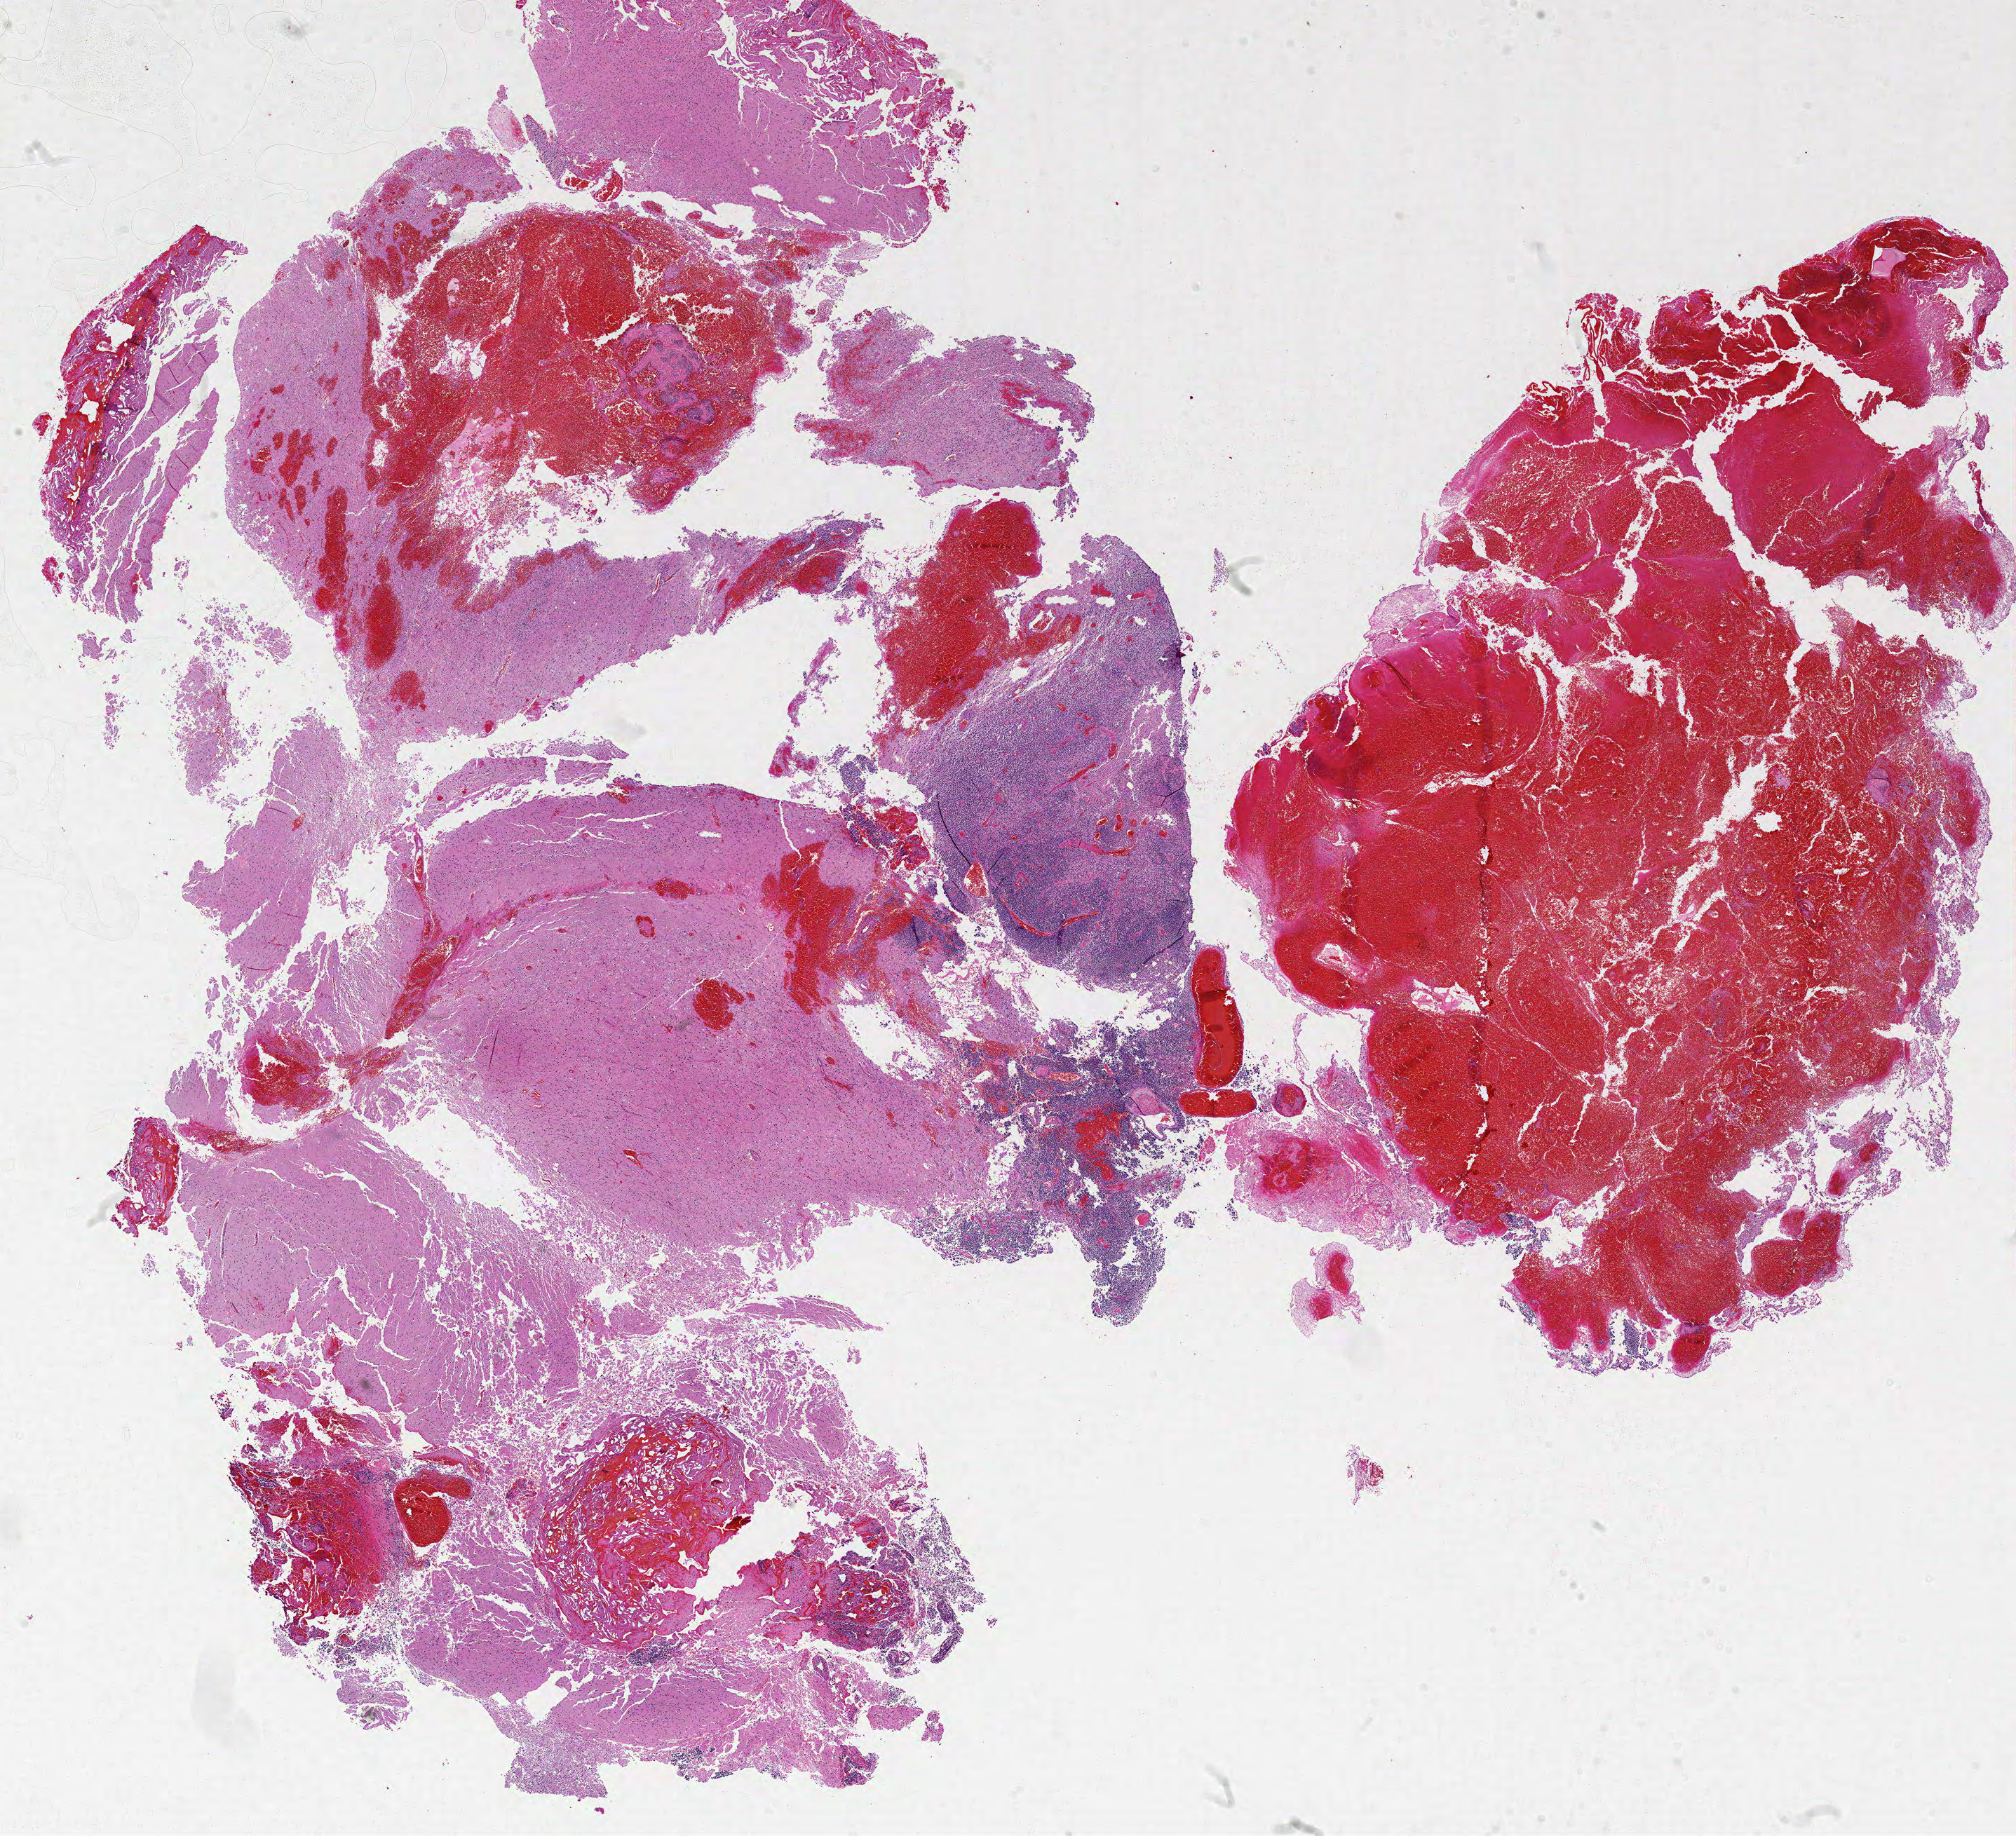
Digitized H&E tissue section (whole slide), whole scanned area (about 23.0 x 20.9 mm) shown as a low-resolution overview, formalin-fixed paraffin-embedded (FFPE) diagnostic section, sample: primary tumour, brain. Patient: male, age at initial diagnosis 46 years.
• histologic diagnosis: Glioblastoma